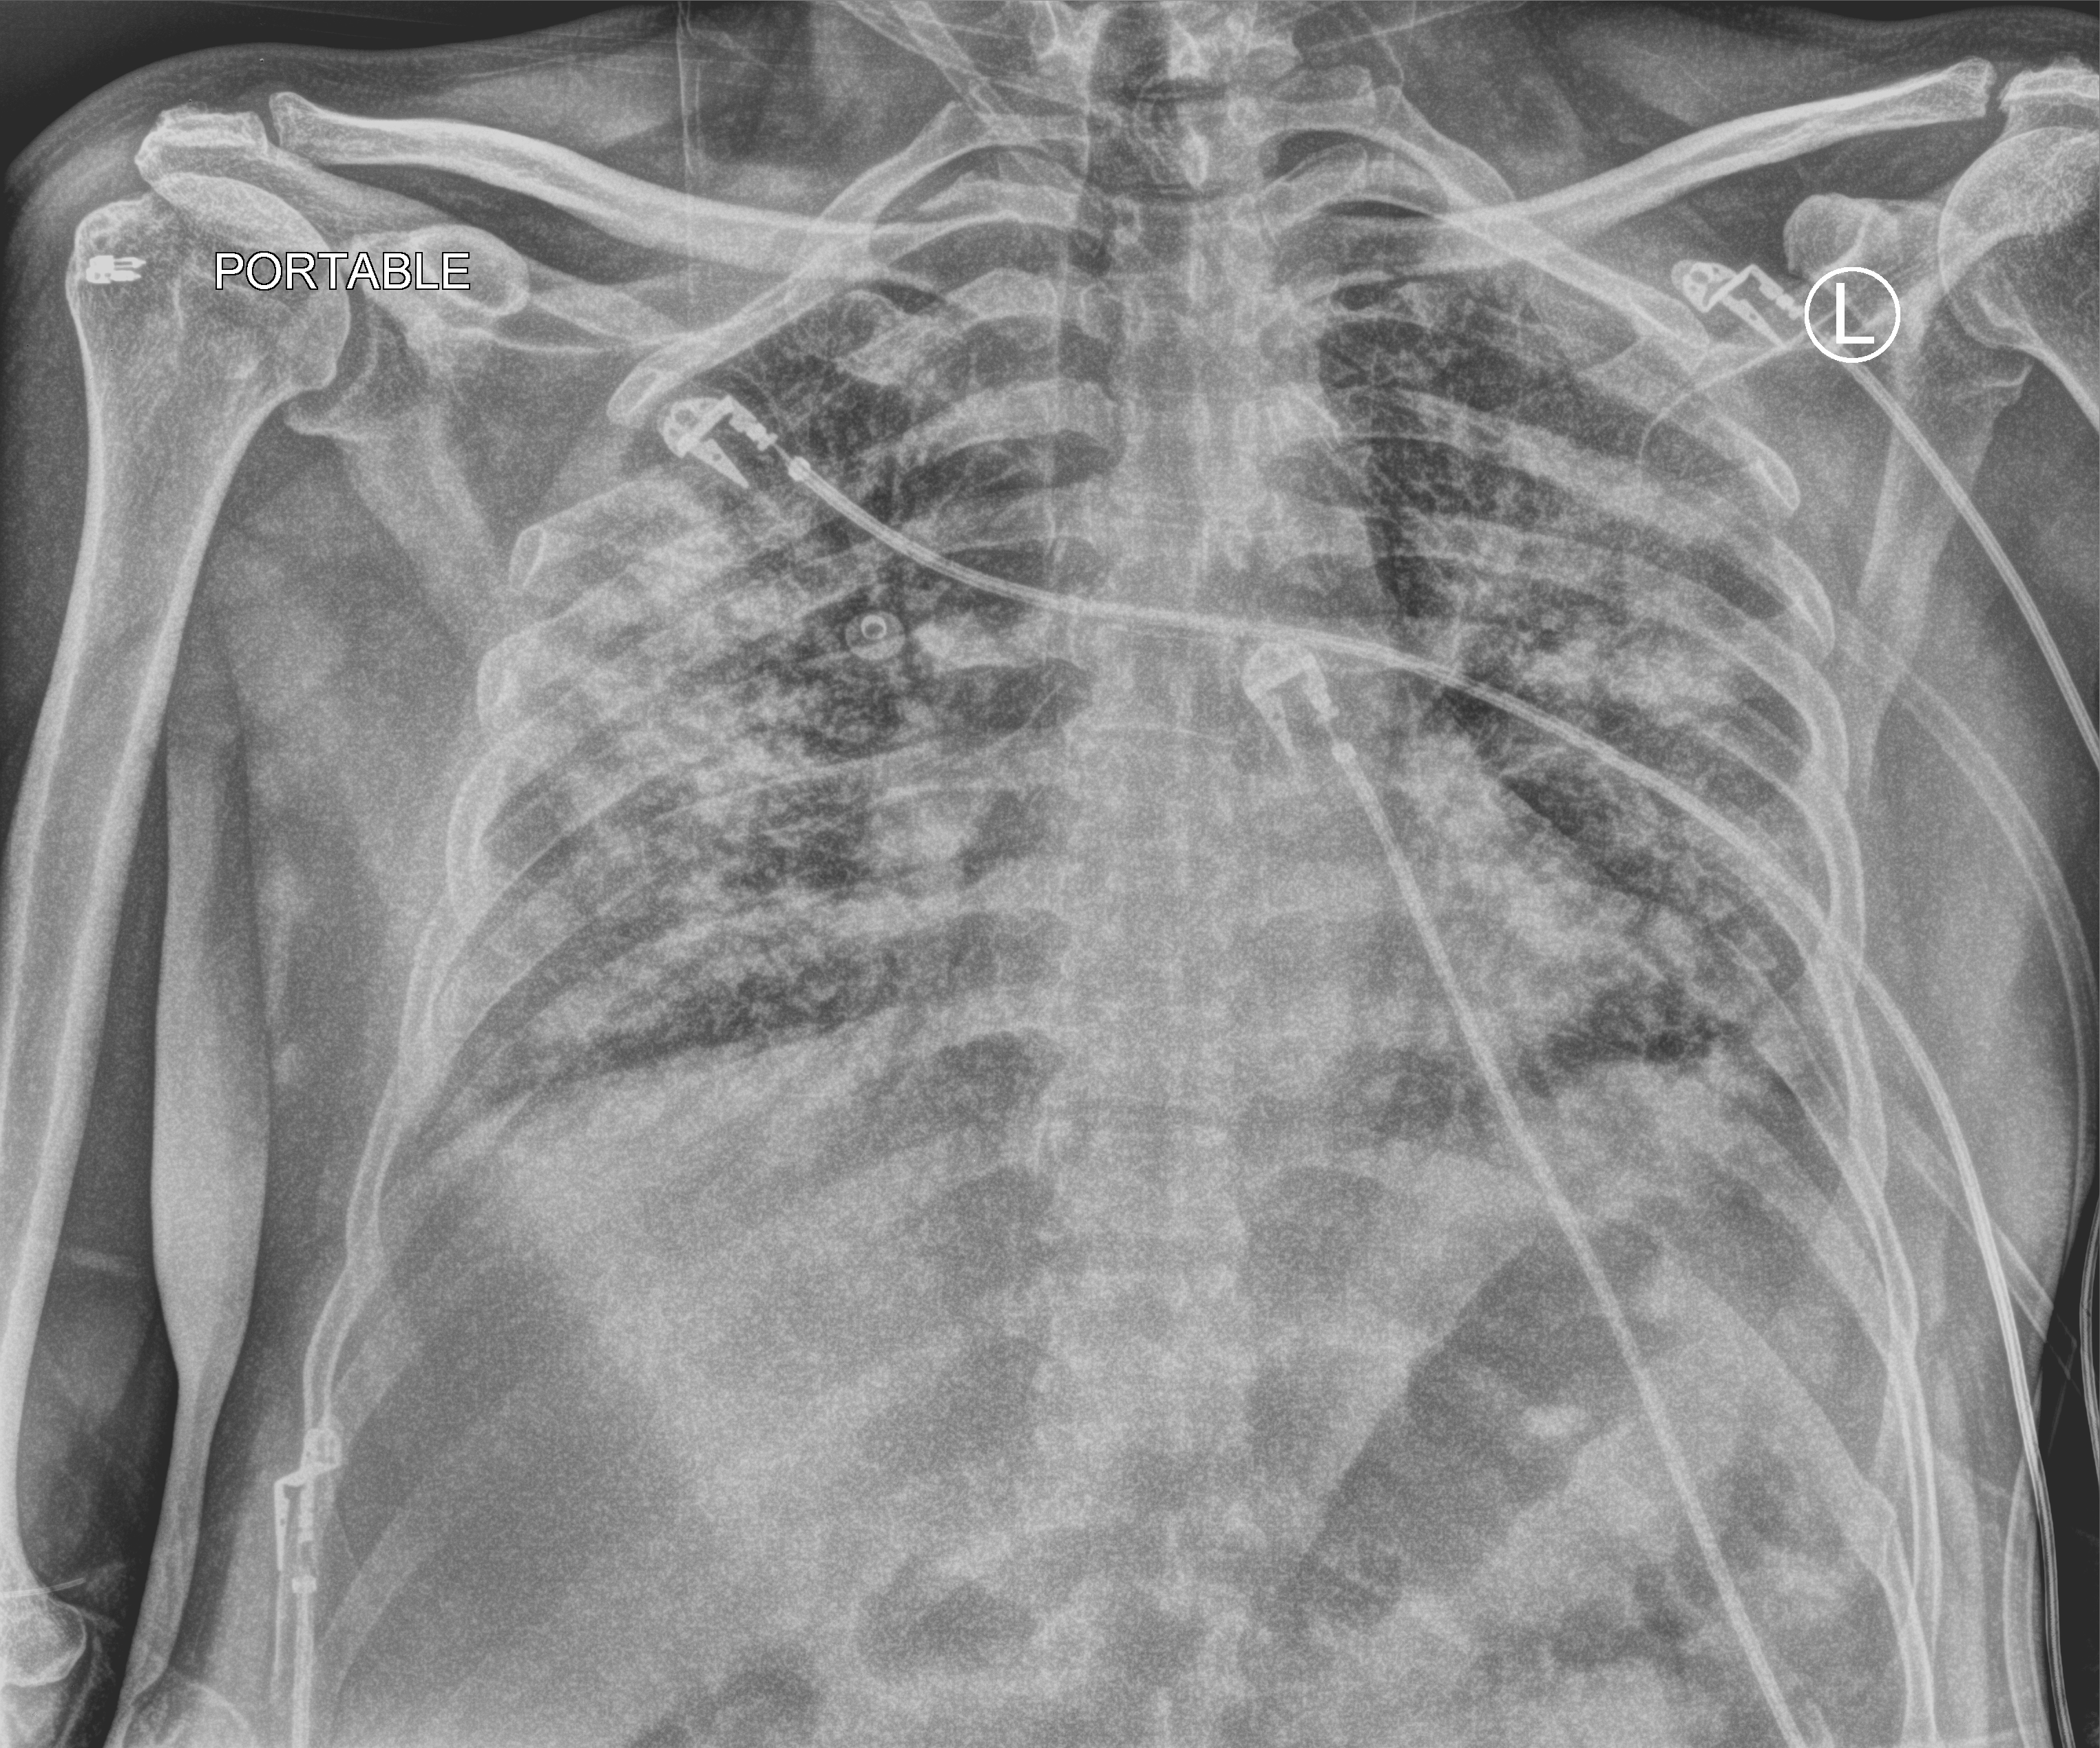
Bedside chest radiograph (computed radiography), anteroposterior (AP) projection. Male patient hospitalised with COVID-19, age 60–74 years.
Admission-level facts for this patient (not findings on this image; timing relative to this image not recorded):
- mechanically ventilated during this hospital stay: yes
- admitted to intensive care during this hospital stay: yes
- COPD (admission record): no